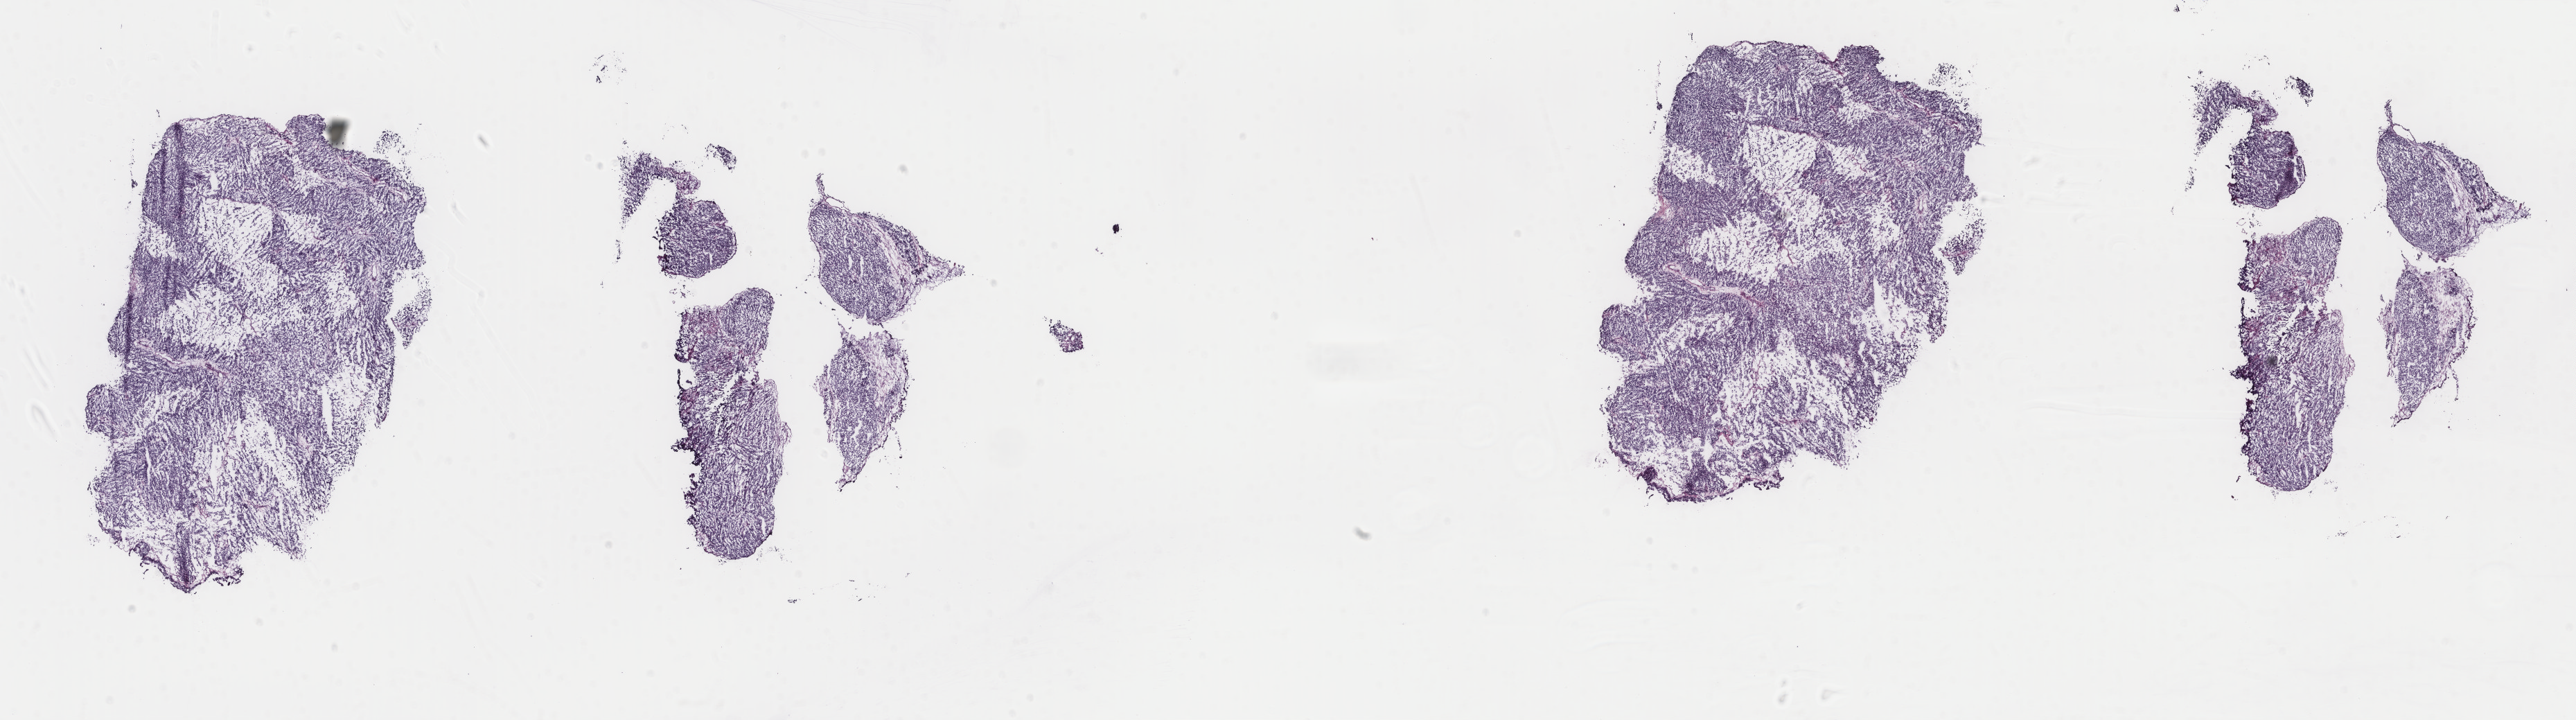
Digitized H&E tissue section (whole slide) — shown as a low-resolution overview of the whole scanned area (about 29.5 x 8.2 mm). Frozen section from the top of the tissue portion. Primary tumour sample from the uterus. Female patient; age at initial diagnosis 75 years. Pathologist review of this section (percent, as recorded): tumour cells 100%, tumour nuclei 80%, normal cells 0%, stromal cells 0%, necrosis 0%. Infiltration values recorded for this section: lymphocyte infiltration 2%, monocyte infiltration 0%, neutrophil infiltration 0%.
Histologic diagnosis: Carcinosarcoma, NOS. FIGO stage: IIIC1.